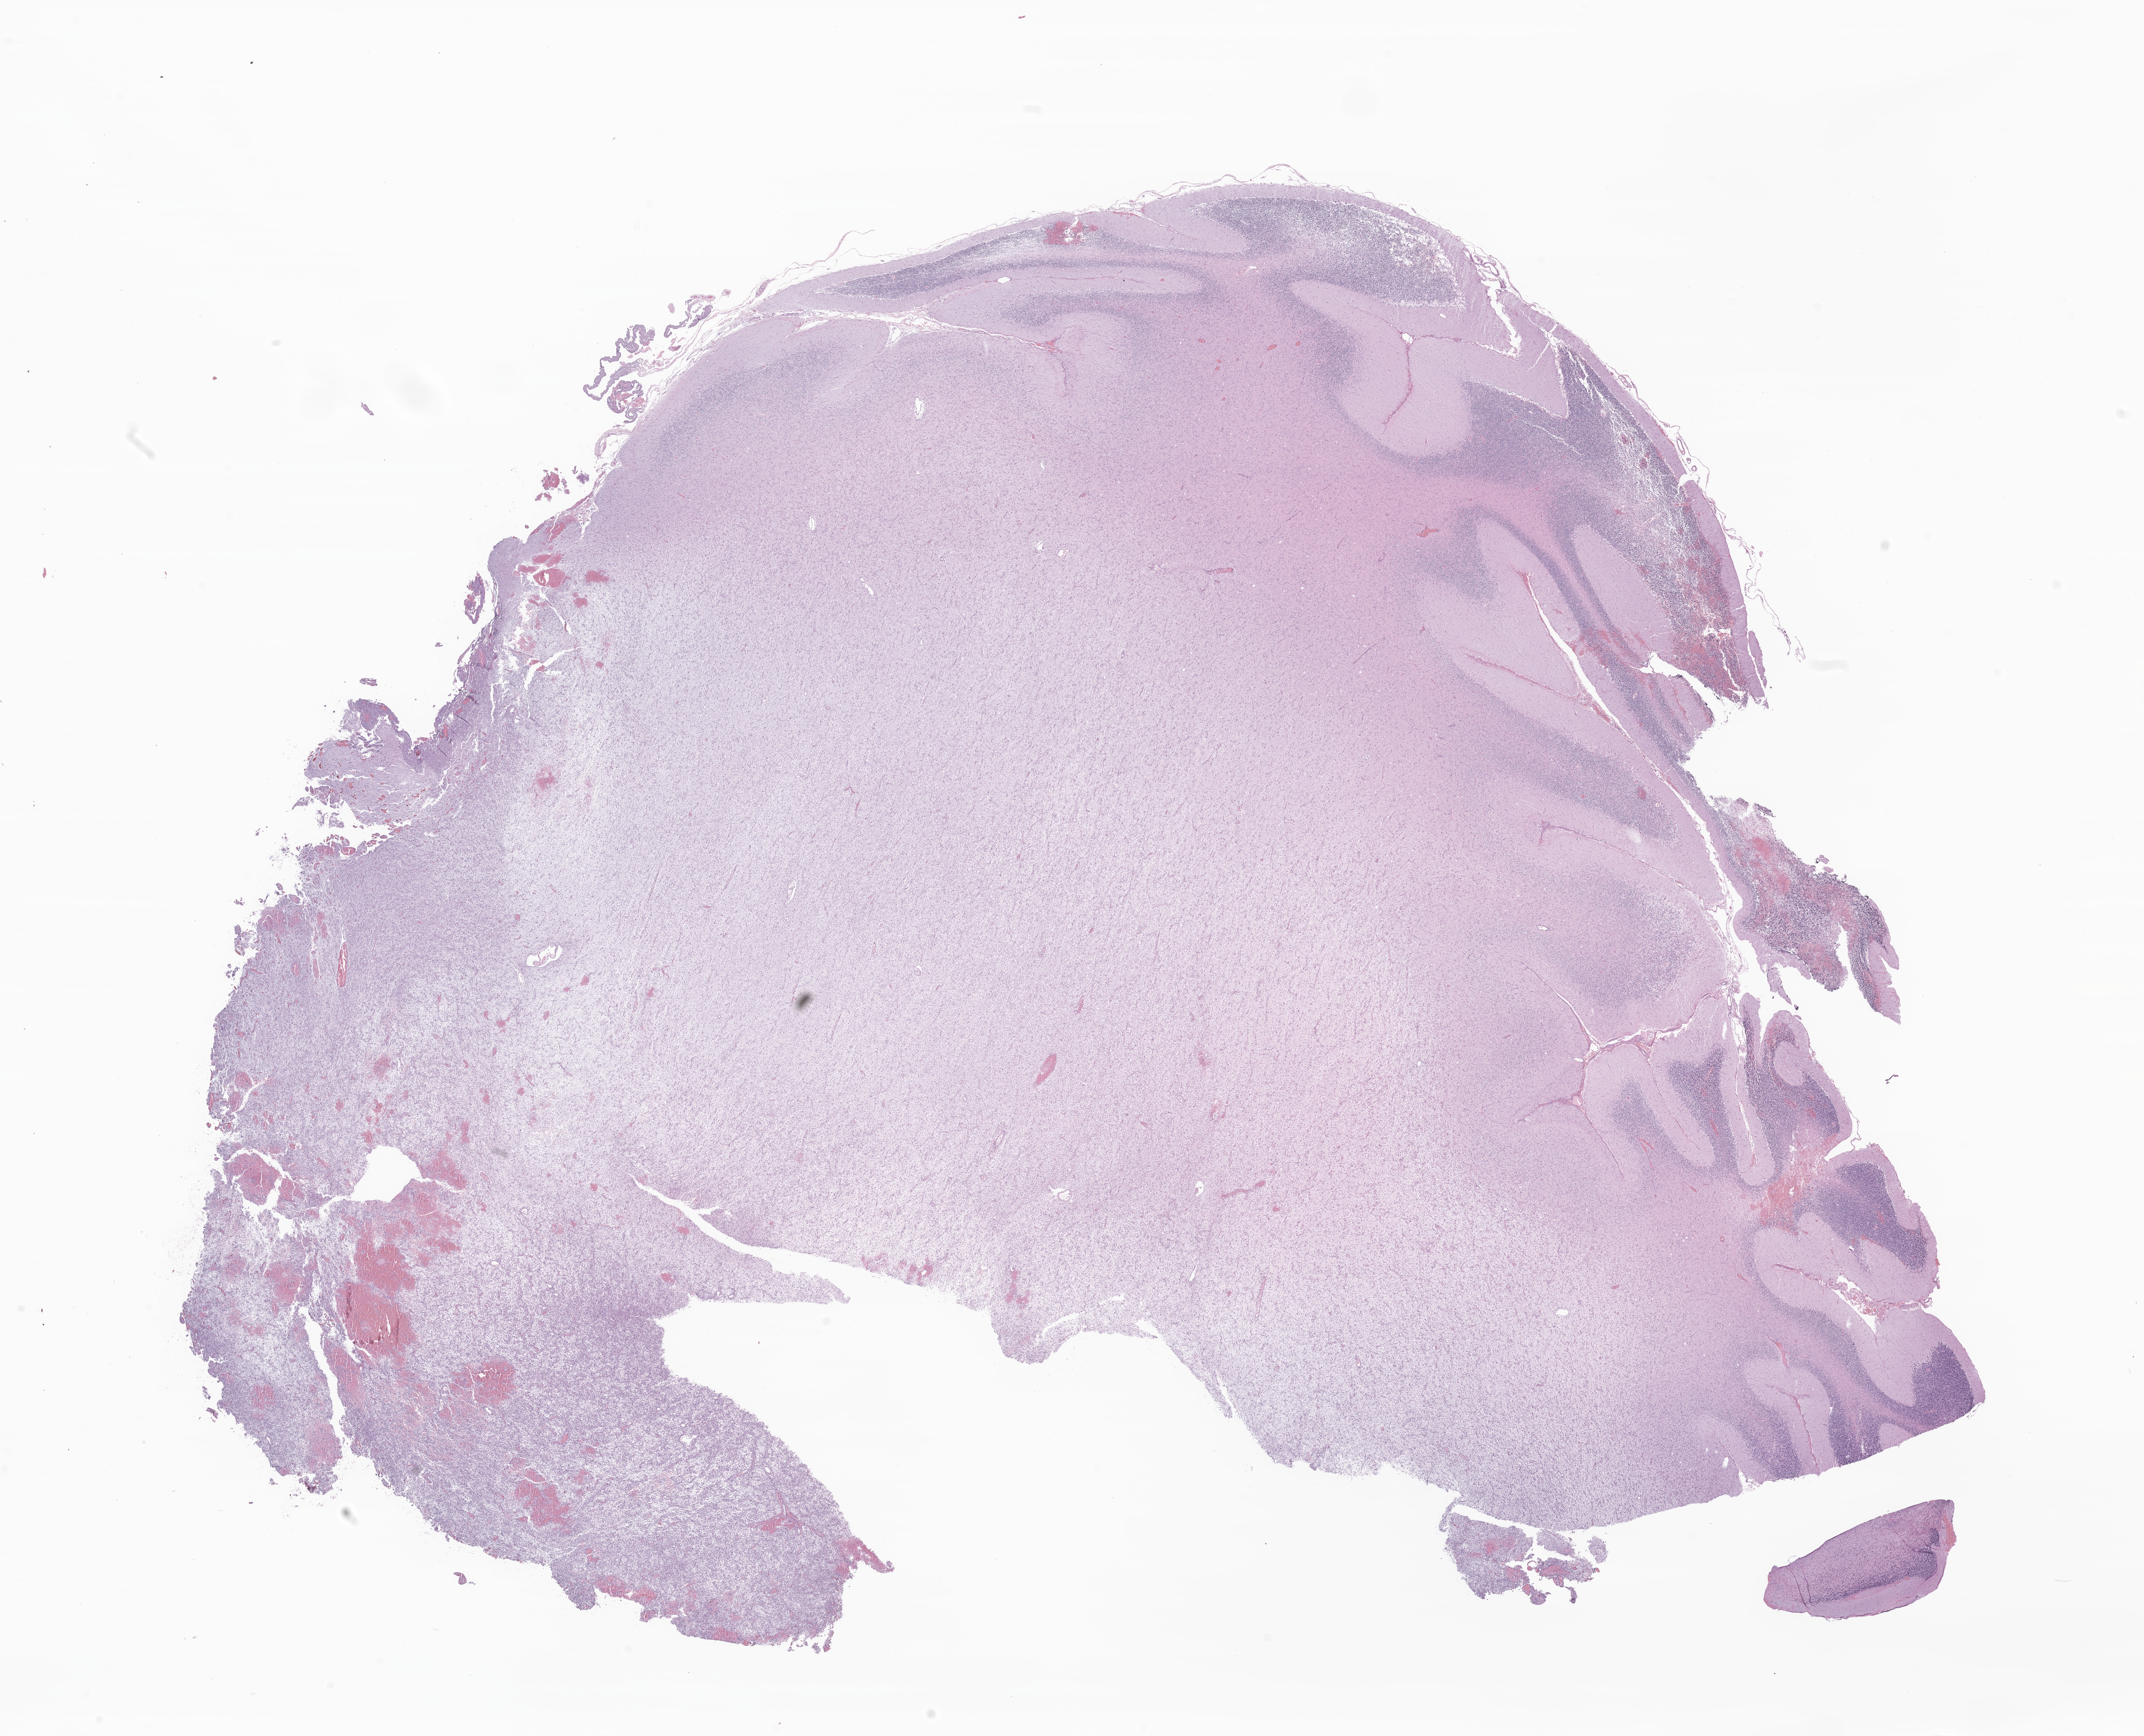
Digitized haematoxylin and eosin-stained section of tumor tissue from the cerebellum, shown as a low-resolution overview of the whole scanned area (about 26.2 x 21.2 mm), formalin-fixed, paraffin-embedded (FFPE) tissue. Male patient, age 860 days (about 2.4 years).
* diagnosis: Glioma, malignant